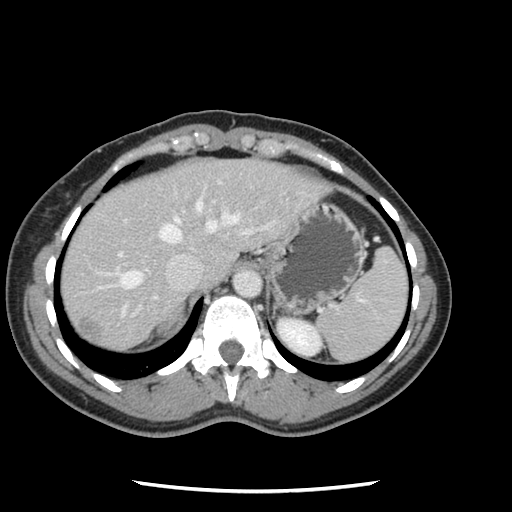
Contrast-enhanced abdominal CT, one axial slice. Soft-tissue window (W 400 / L 40 HU). 2.5 mm slice thickness. 512 × 512 image matrix, field of view 330 × 330 mm. Female patient, age 43 years. From the clinical record (not read from this slice): diagnosis: colorectal cancer liver metastases, imaged before liver resection; multiple liver metastases: yes; largest metastasis: 3.4 cm.
Outlined on this slice (expert manual segmentation):
- hepatic veins: bounding box <117,201,241,315> (left, top, right, bottom; pixels)
- liver: <62,159,325,352>
- planned liver remnant (the part of the liver to remain after resection): <62,168,195,308>
- portal vein (with intrahepatic branches): <117,219,271,316>
- liver metastasis: <74,318,101,344>